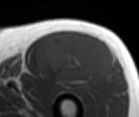
MRI of an extremity soft-tissue mass, one axial slice; position 59 of 86 along the scan axis; MR volume resampled by the dataset authors to the PET/CT grid (not the native acquisition matrix); 3.27 mm slice thickness; 139 × 117 image matrix, field of view 136 × 114 mm. Male patient. Case-level facts recorded for this patient, not image findings: histological type: extraskeletal osteosarcoma; grade: high; site of the primary tumour: thigh.
Annotated regions visible in this slice (expert contour drawn on MRI and transferred to this co-registered scan by the dataset authors):
- gross tumour volume (mass): box from (x=36, y=32) to (x=112, y=83) px